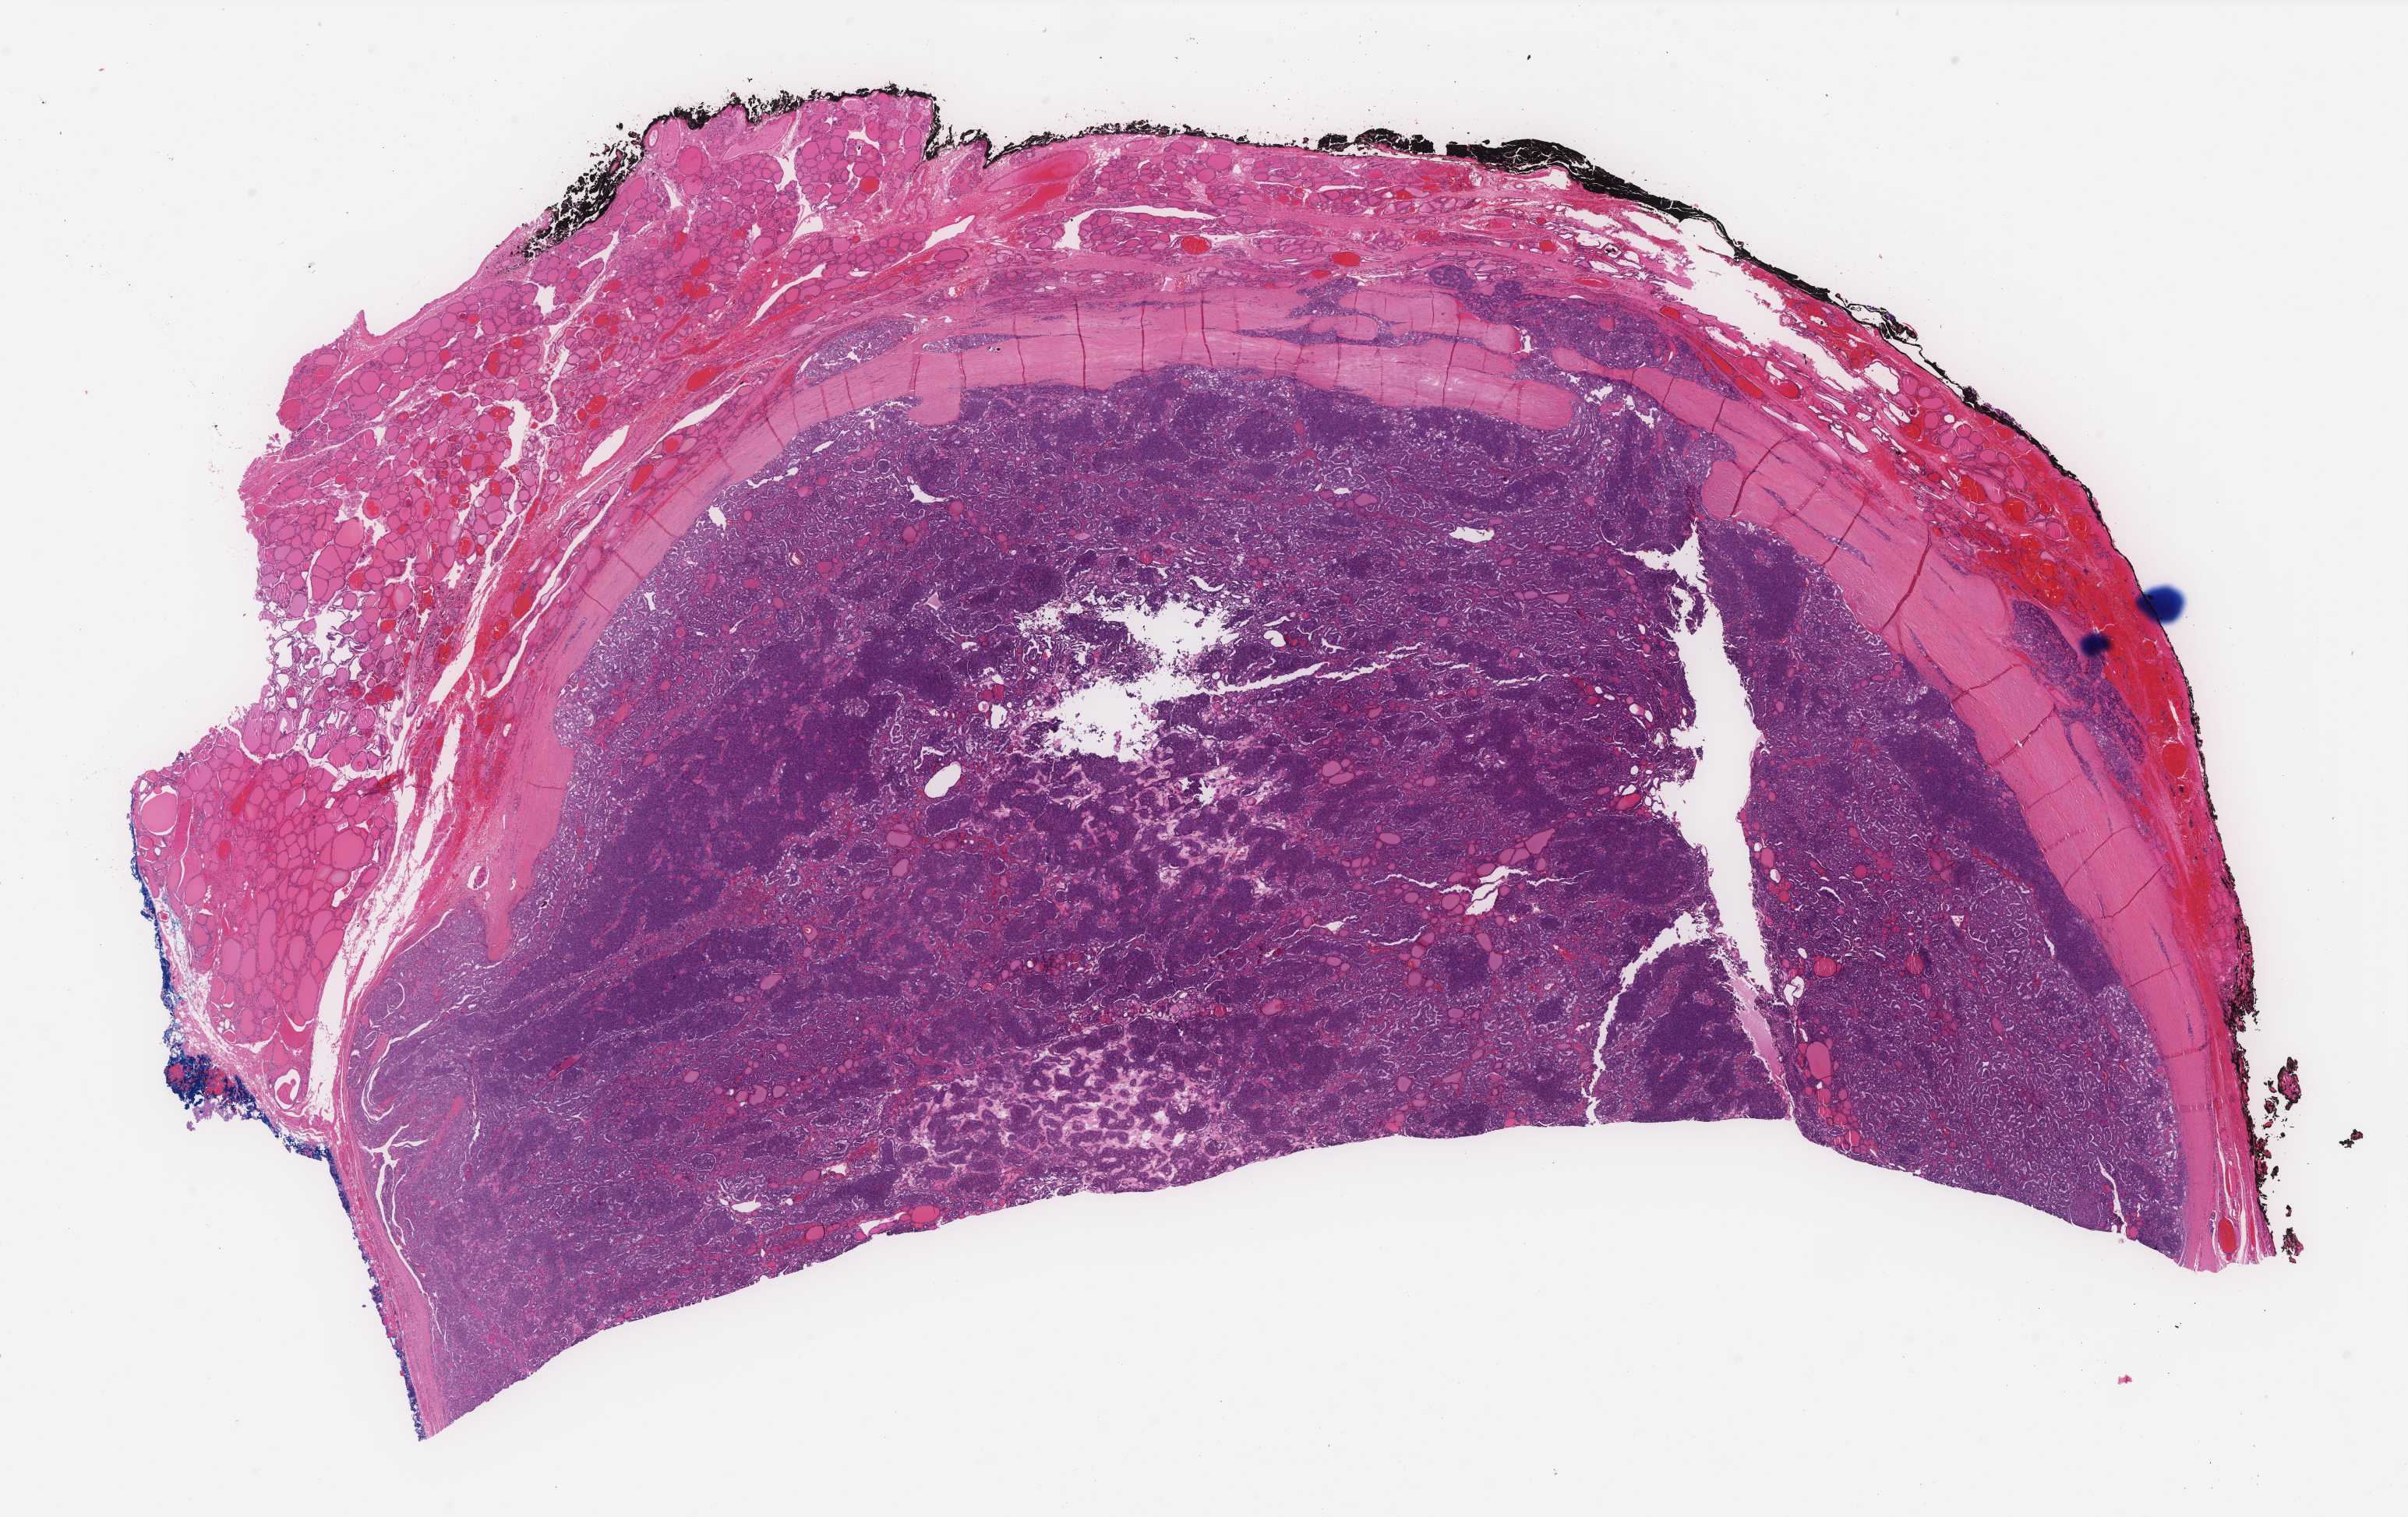
Digitized H&E-stained tissue section (whole slide) — shown as a low-resolution overview of the whole scanned area (about 24.8 x 15.6 mm). FFPE section. Primary tumour sample from the thyroid. Female, age 30 years at initial diagnosis.
AJCC pathologic stage: I (7th edition). TNM: T3 N1b MX. Pathologic diagnosis: Papillary adenocarcinoma, NOS (thyroid gland). Laterality: bilateral.